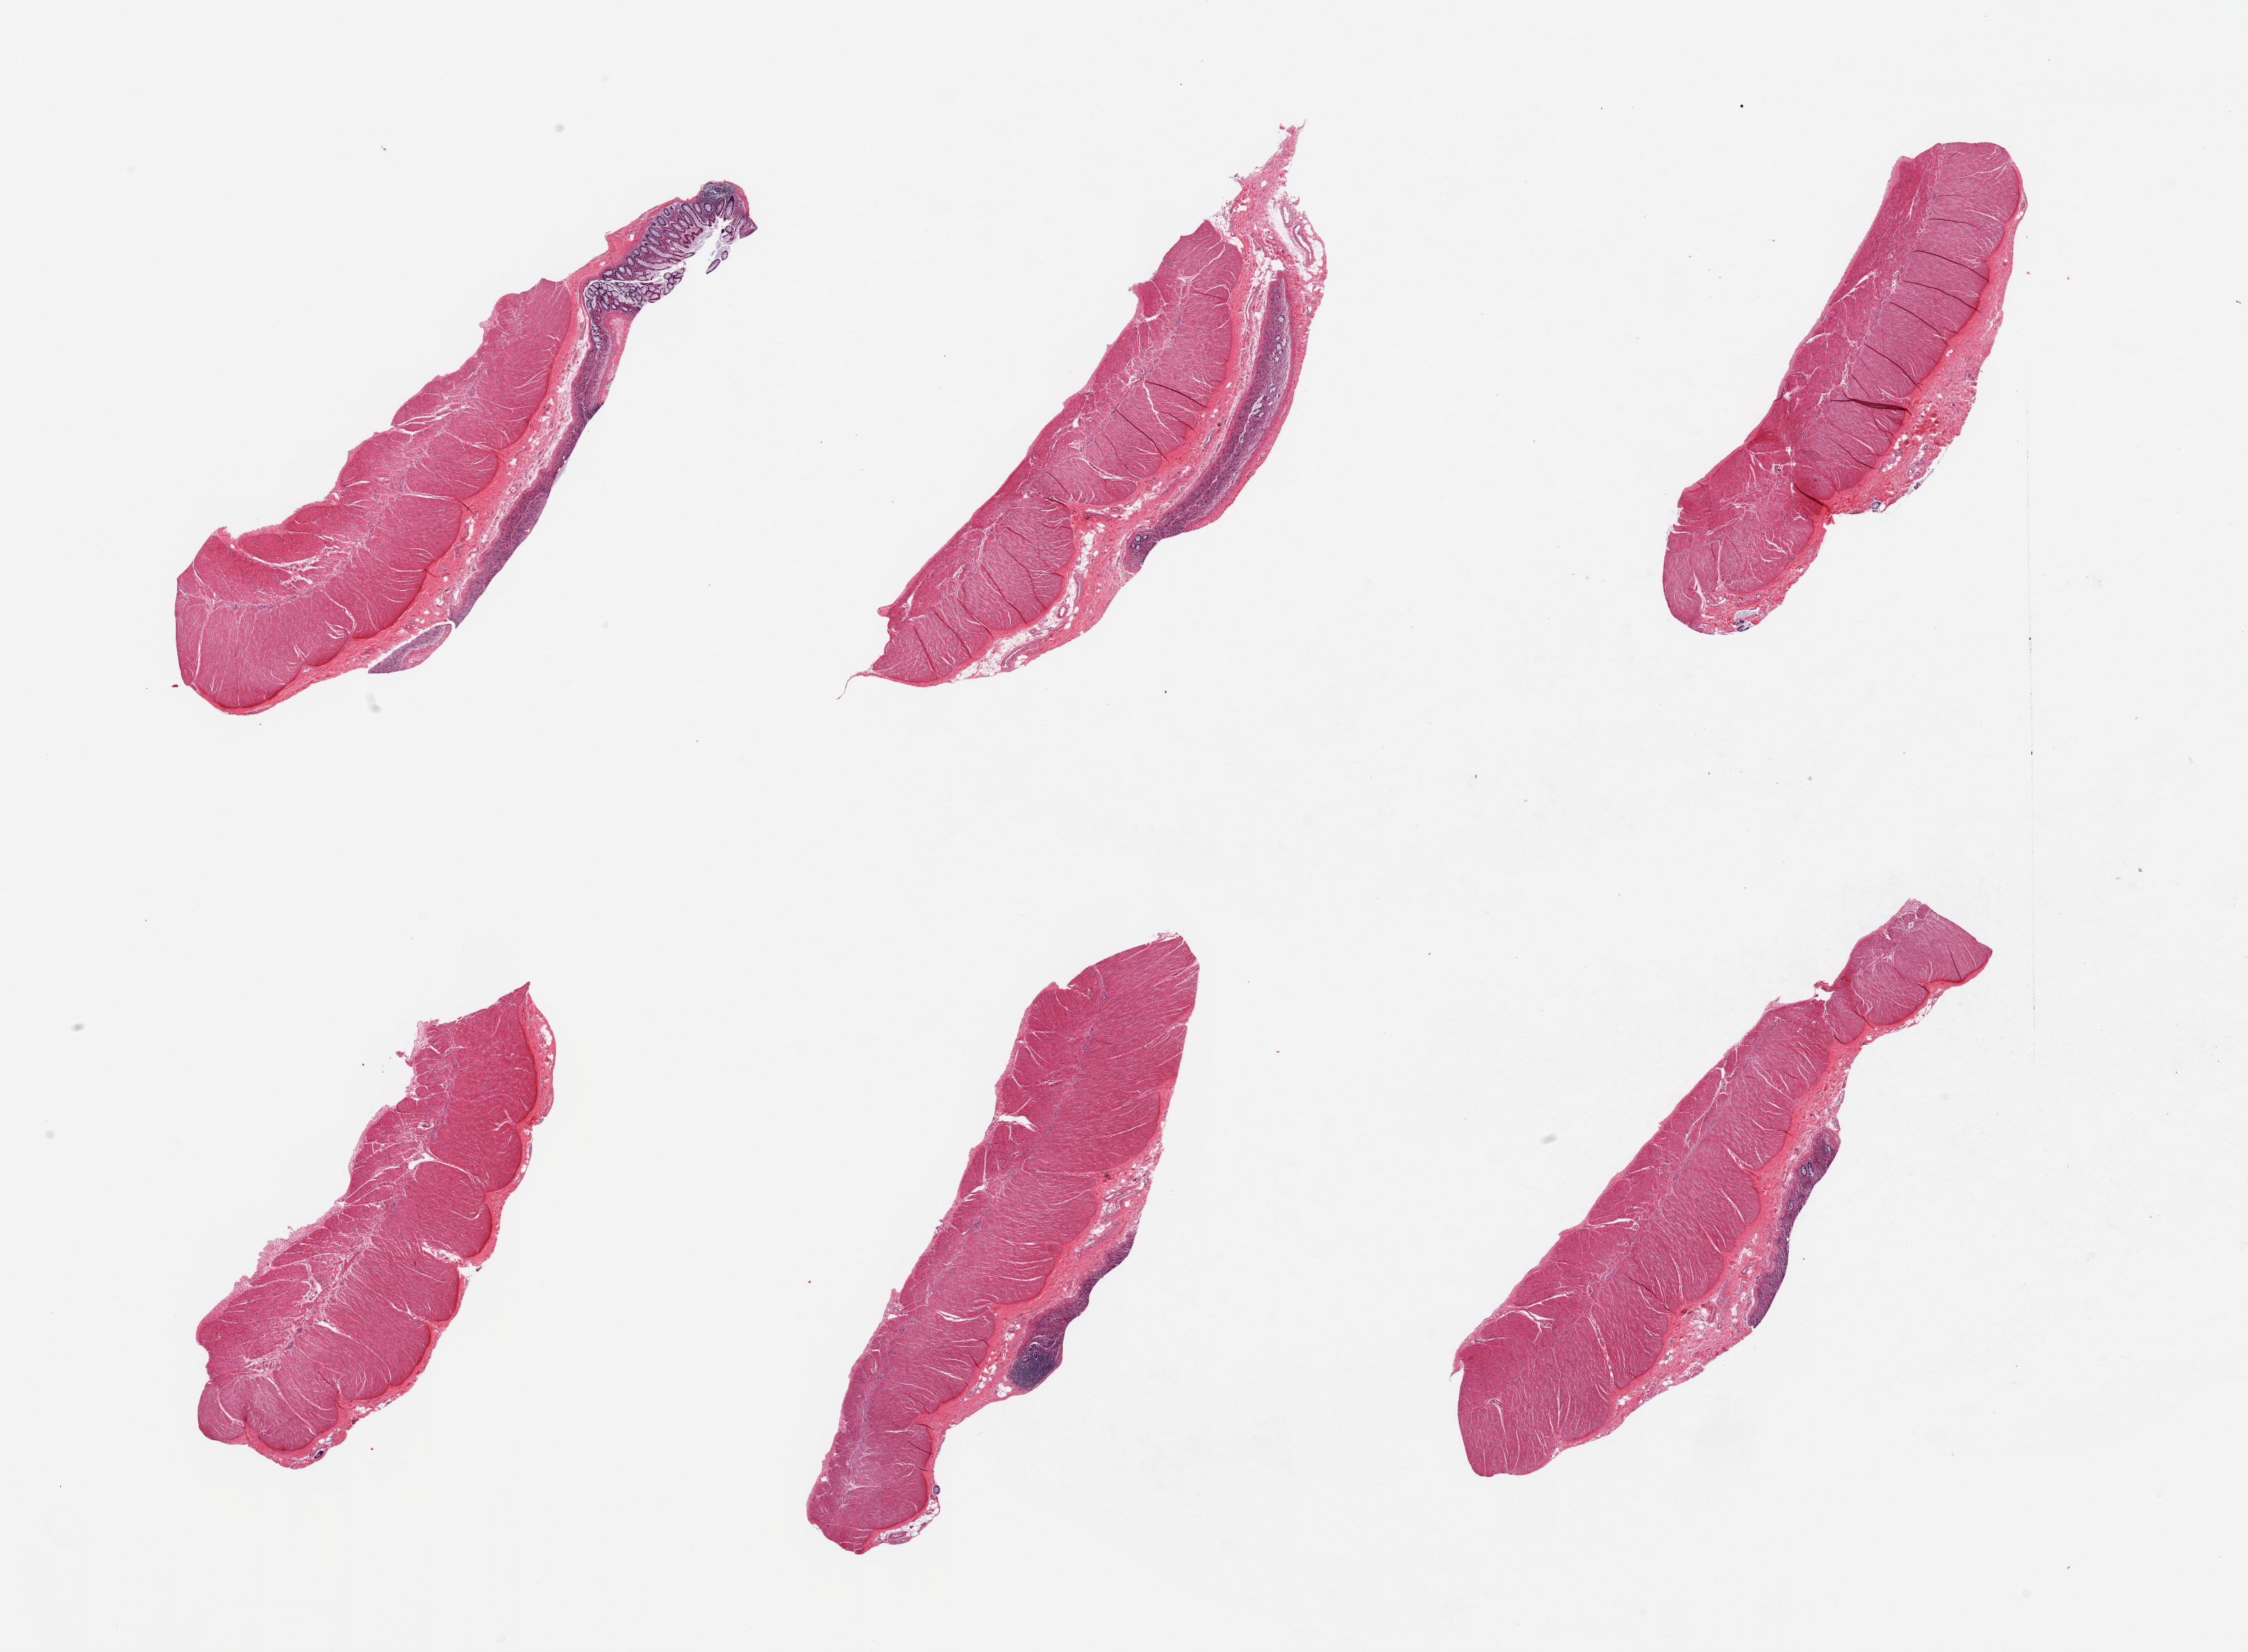
H&E whole-slide image, shown as a low-resolution overview of the whole scanned area (about 25.6 x 18.8 mm), PAXgene-fixed, paraffin-embedded tissue, section of sigmoid colon (target tissue), tissue donor sample.
* review note (as recorded): 6 pieces; mucosa occupies 10% to 20% of 4 of 6 pieces